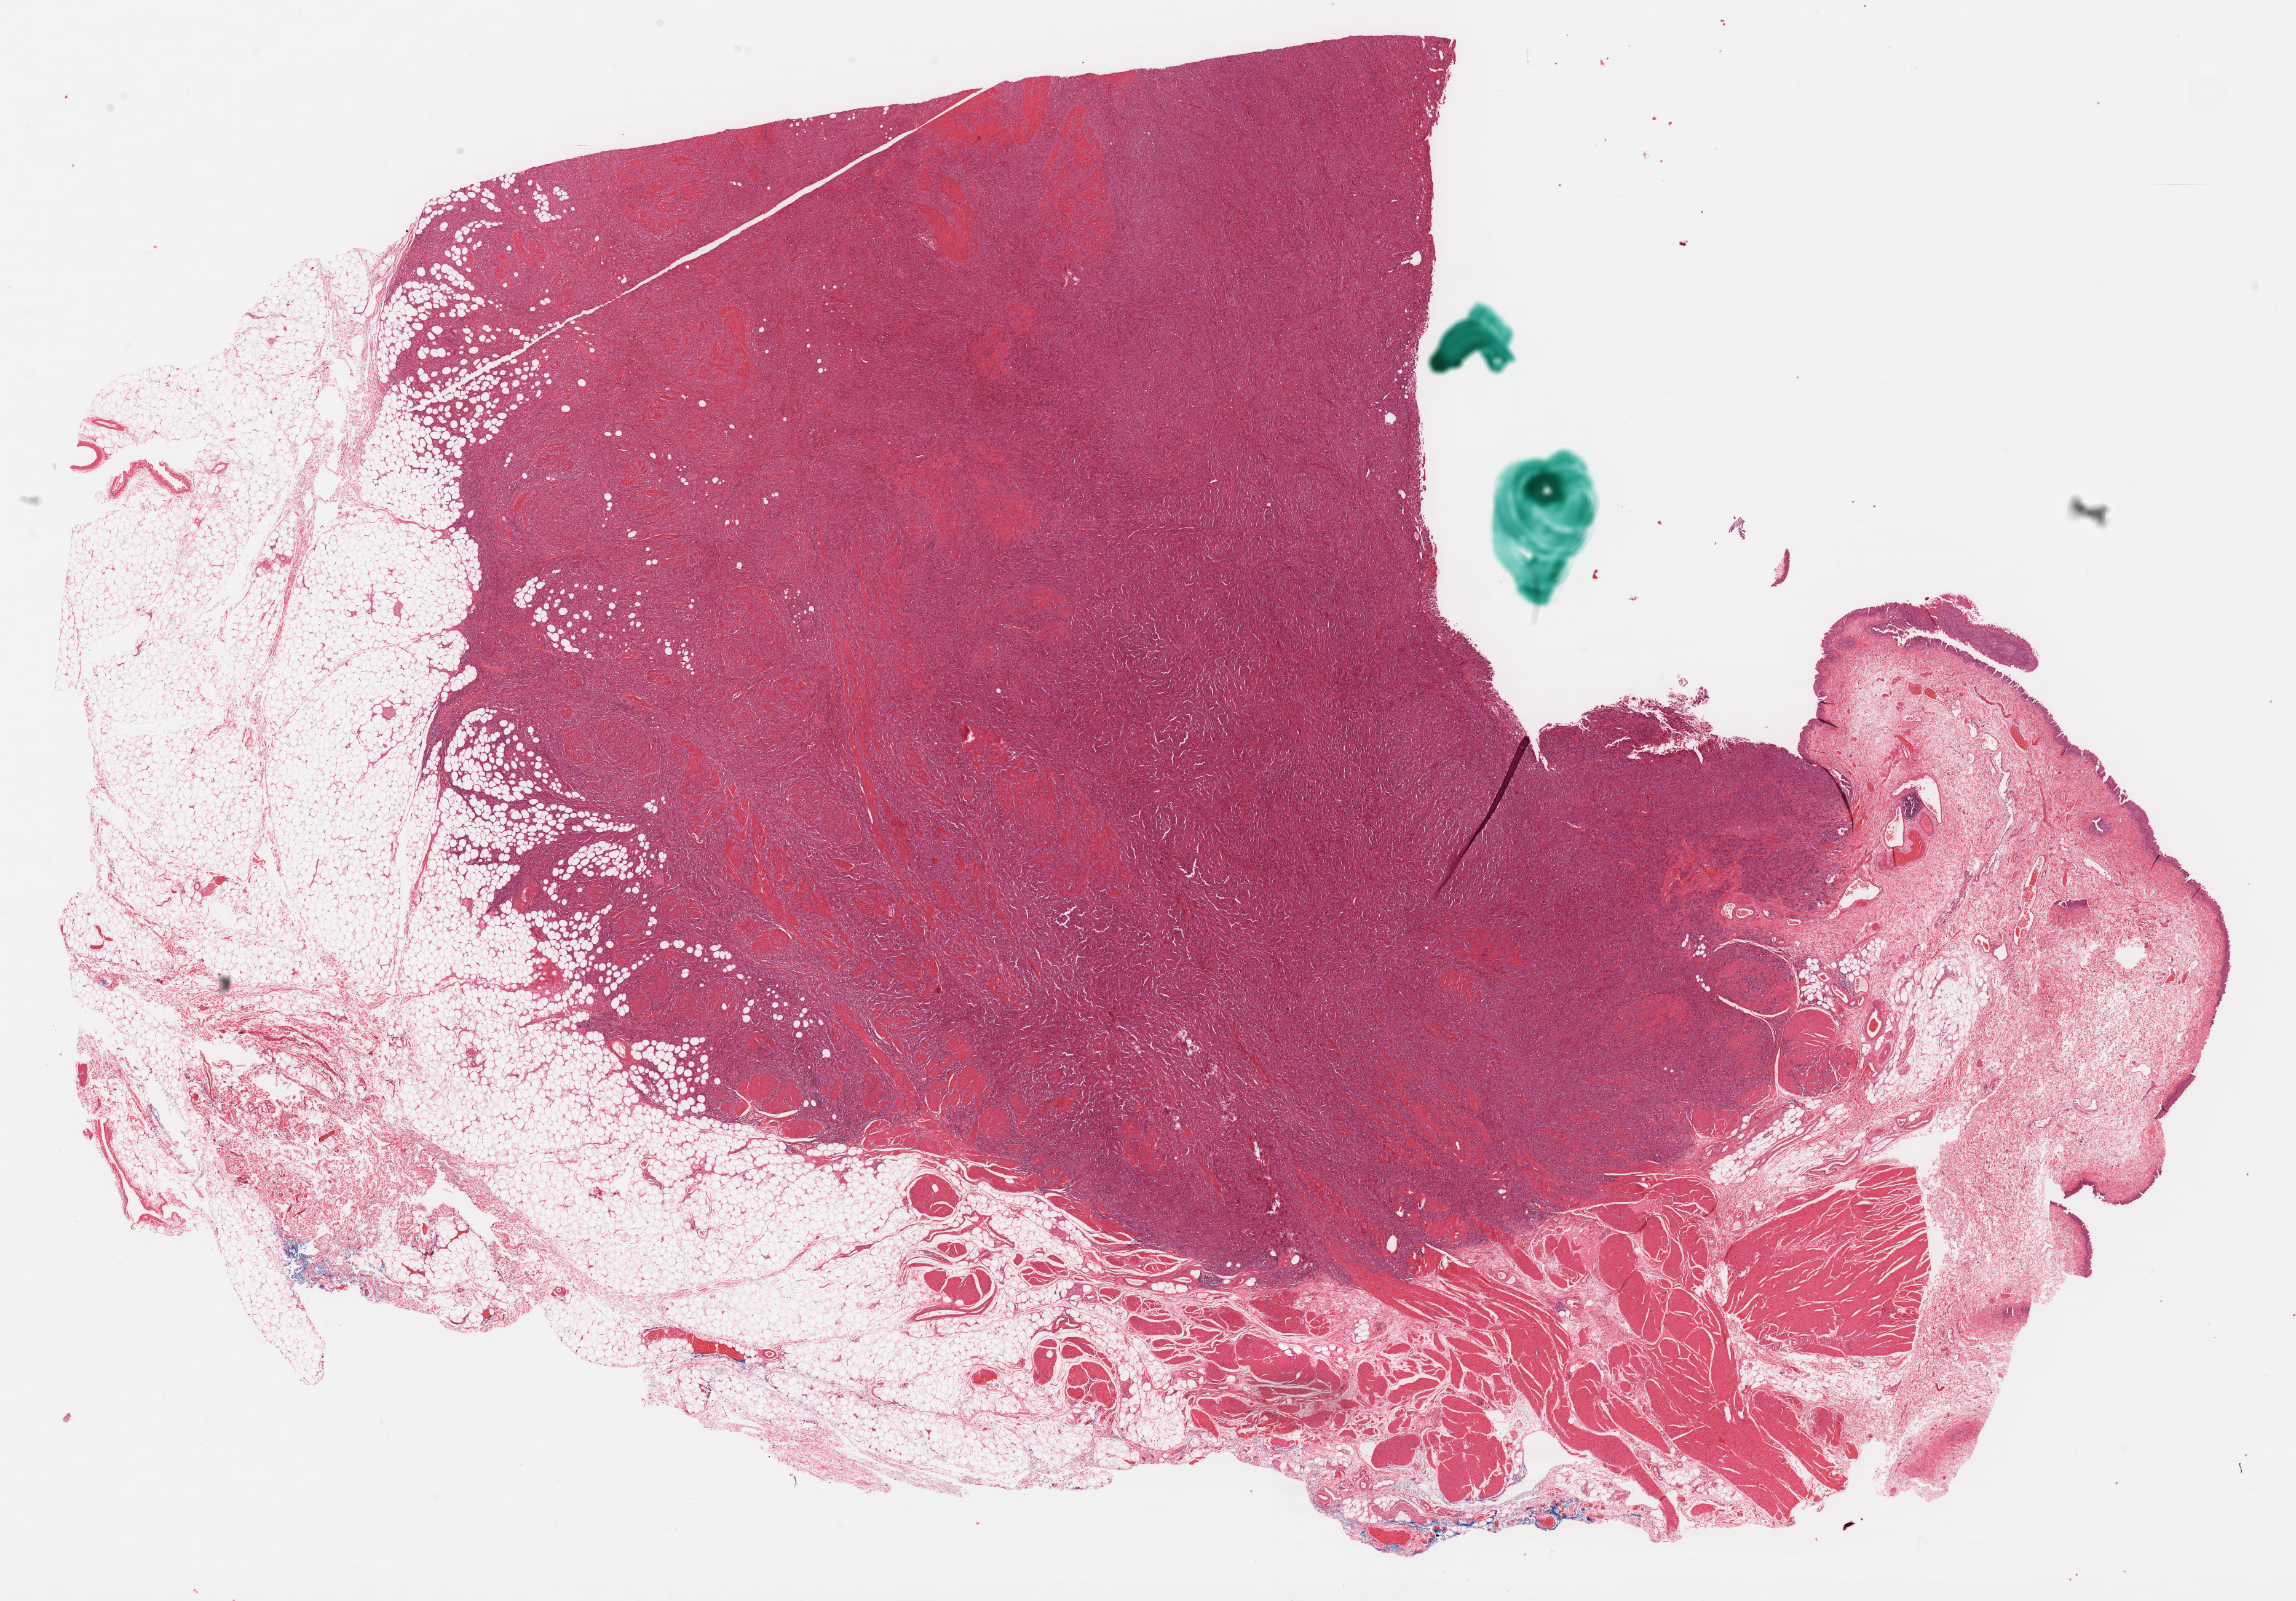
Whole-slide histology image, H&E, shown as a low-resolution overview of the whole scanned area (about 30.2 x 21.1 mm). Formalin-fixed paraffin-embedded (FFPE) diagnostic section. Primary tumour sample from the bladder. Male, age 71 years at initial diagnosis. Histologic grade: high grade.
TNM: T3 NX MX. Pathologic diagnosis: Transitional cell carcinoma (lateral wall of bladder). AJCC pathologic stage: III (6th edition).